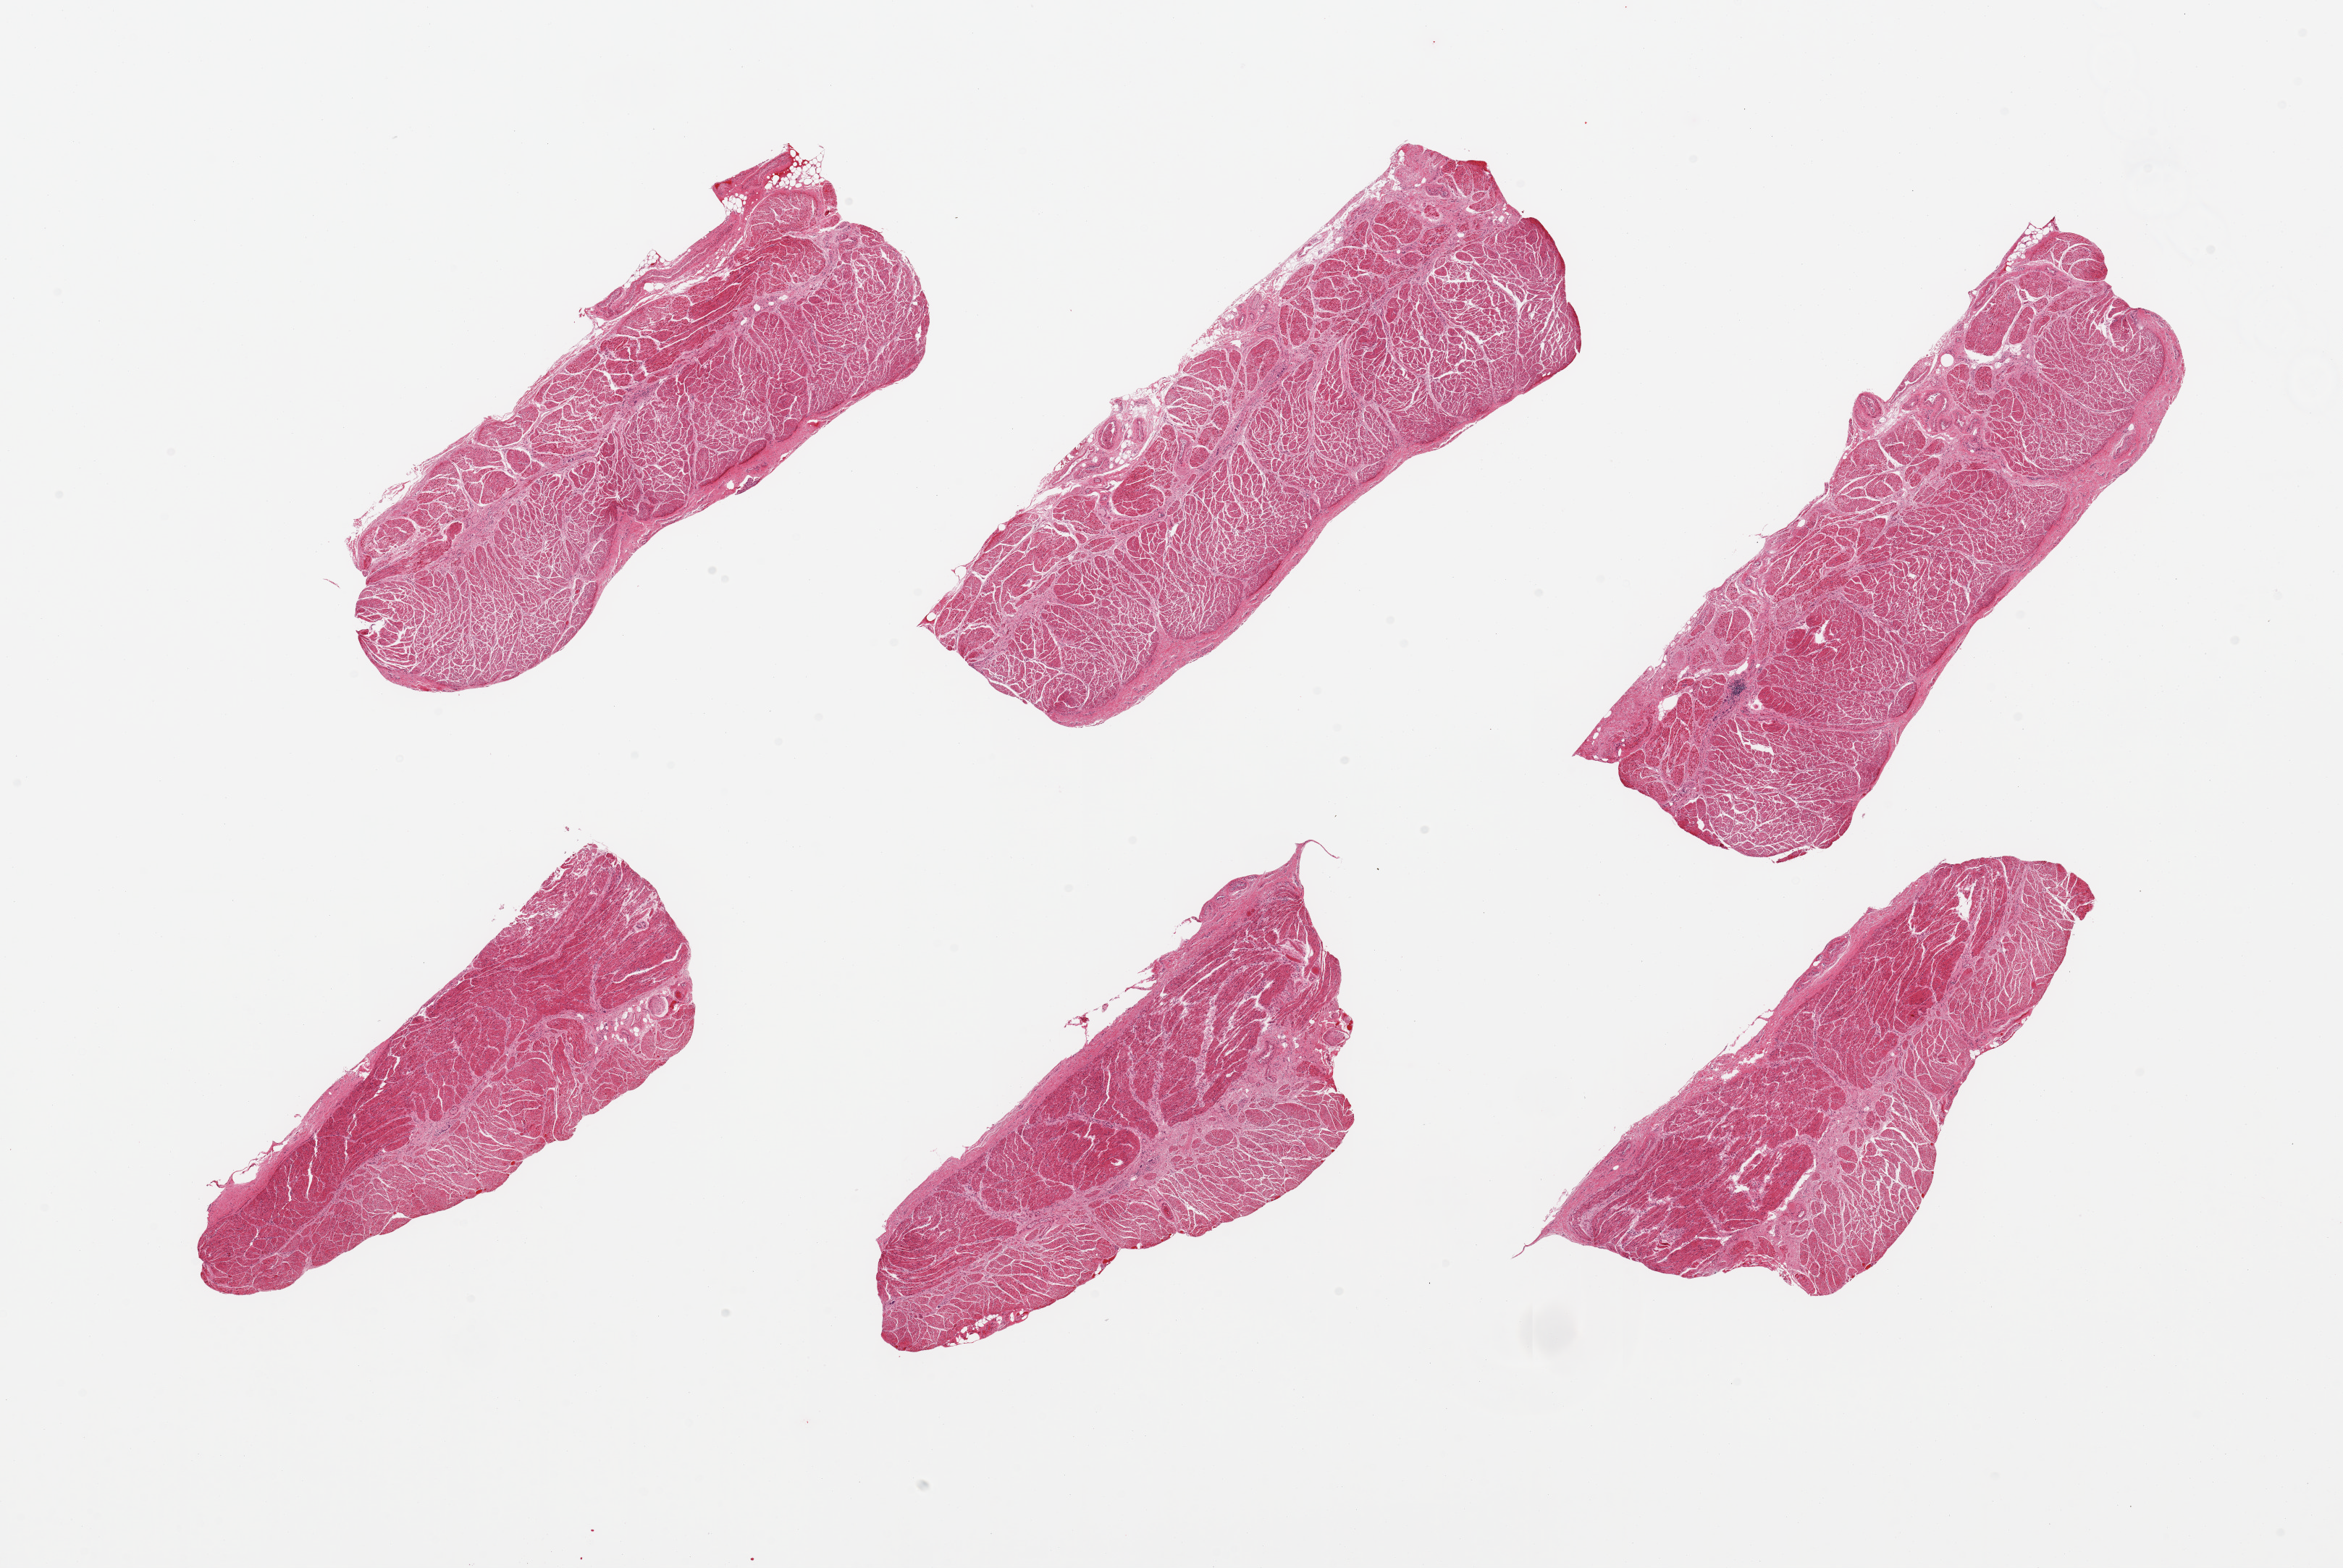
Hematoxylin and eosin (H&E) whole-slide image — a low-resolution overview of the entire scanned area, about 25.6 x 17.1 mm (from a 20x scan). PAXgene-fixed, paraffin-embedded tissue. Sampled site (target tissue): esophageal muscle. Donor tissue sample. Donor sex: female.
Reviewer comment on this tissue sample: 6 pieces; well dissected.